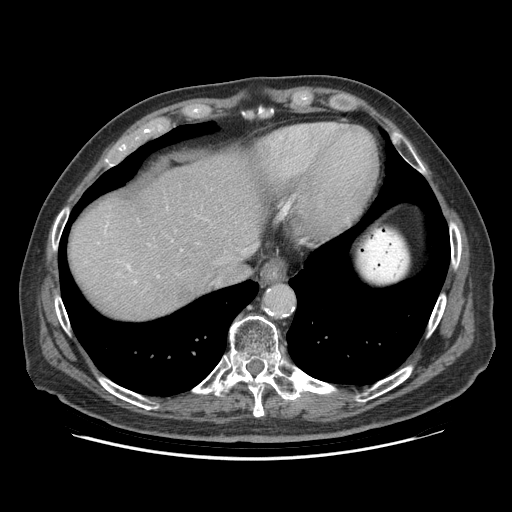
Contrast-enhanced abdominal CT (liver protocol), one axial slice; position 77 of 95 along the scan axis; 140 kVp; soft-tissue window (W 400 / L 40 HU); 2.5 mm slice thickness; 512 × 512 image matrix, field of view 400 × 400 mm. From the clinical record (not read from this slice): diagnosis: hepatocellular carcinoma (patient treated with transarterial chemoembolisation; whether this scan precedes or follows treatment is not stated here); TNM stage (as recorded): Stage-IVB; Child-Pugh class: A; tumour differentiation: well differentiated.
Outlined on this slice (semi-automatic segmentation, software-assisted and operator-edited):
- liver parenchyma outside the tumour (the mass and vessels are separate outlines, so this box may not span the whole liver): bounding box [x1, y1, x2, y2] px = [68, 154, 262, 318]
- liver vessels: [127, 265, 130, 269]